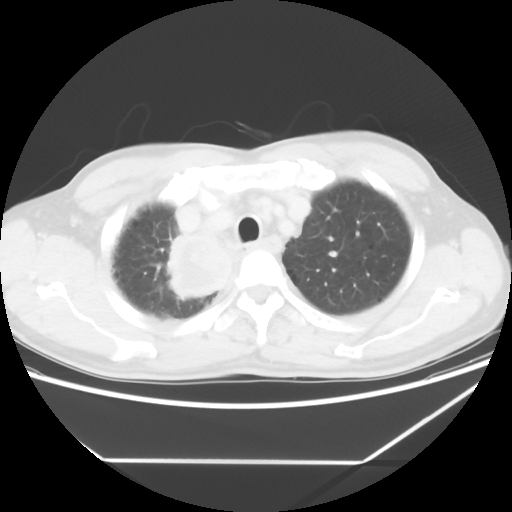
Chest CT, one axial slice. Slice 50 of 60 in the series (ordered by position). Reconstruction kernel STANDARD. 120 kVp. Lung window (W 1500 / L -600 HU). 5 mm slice thickness. 512 × 512 image matrix. Male patient, age 58 years. From the clinical record (not read from this slice): clinical TNM (as recorded): T2 N2 M0.
Structures marked on this image (rectangle marked by the reading radiologist):
- lung tumour (recorded histology: squamous cell carcinoma): bounding box <159,218,237,313> (left, top, right, bottom; pixels)